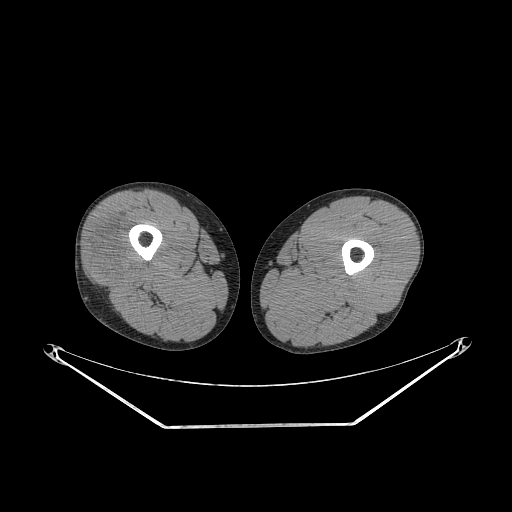
CT of an extremity soft-tissue mass (from a PET/CT study), one axial slice; slice 228 of 267 in the series (ordered by position); reconstruction kernel STANDARD; soft-tissue window (W 400 / L 40 HU); 3.75 mm slice thickness; 512 × 512 image matrix, field of view 500 × 500 mm. Male patient. Case-level facts recorded for this patient, not image findings: histological type: poorly differentiated synovial sarcoma; grade: high; site of the primary tumour: right buttock.
Outlined on this slice (expert contour drawn on MRI and transferred to this co-registered scan by the dataset authors):
- gross tumour volume including surrounding oedema: bounding box <91,230,136,282> (left, top, right, bottom; pixels)